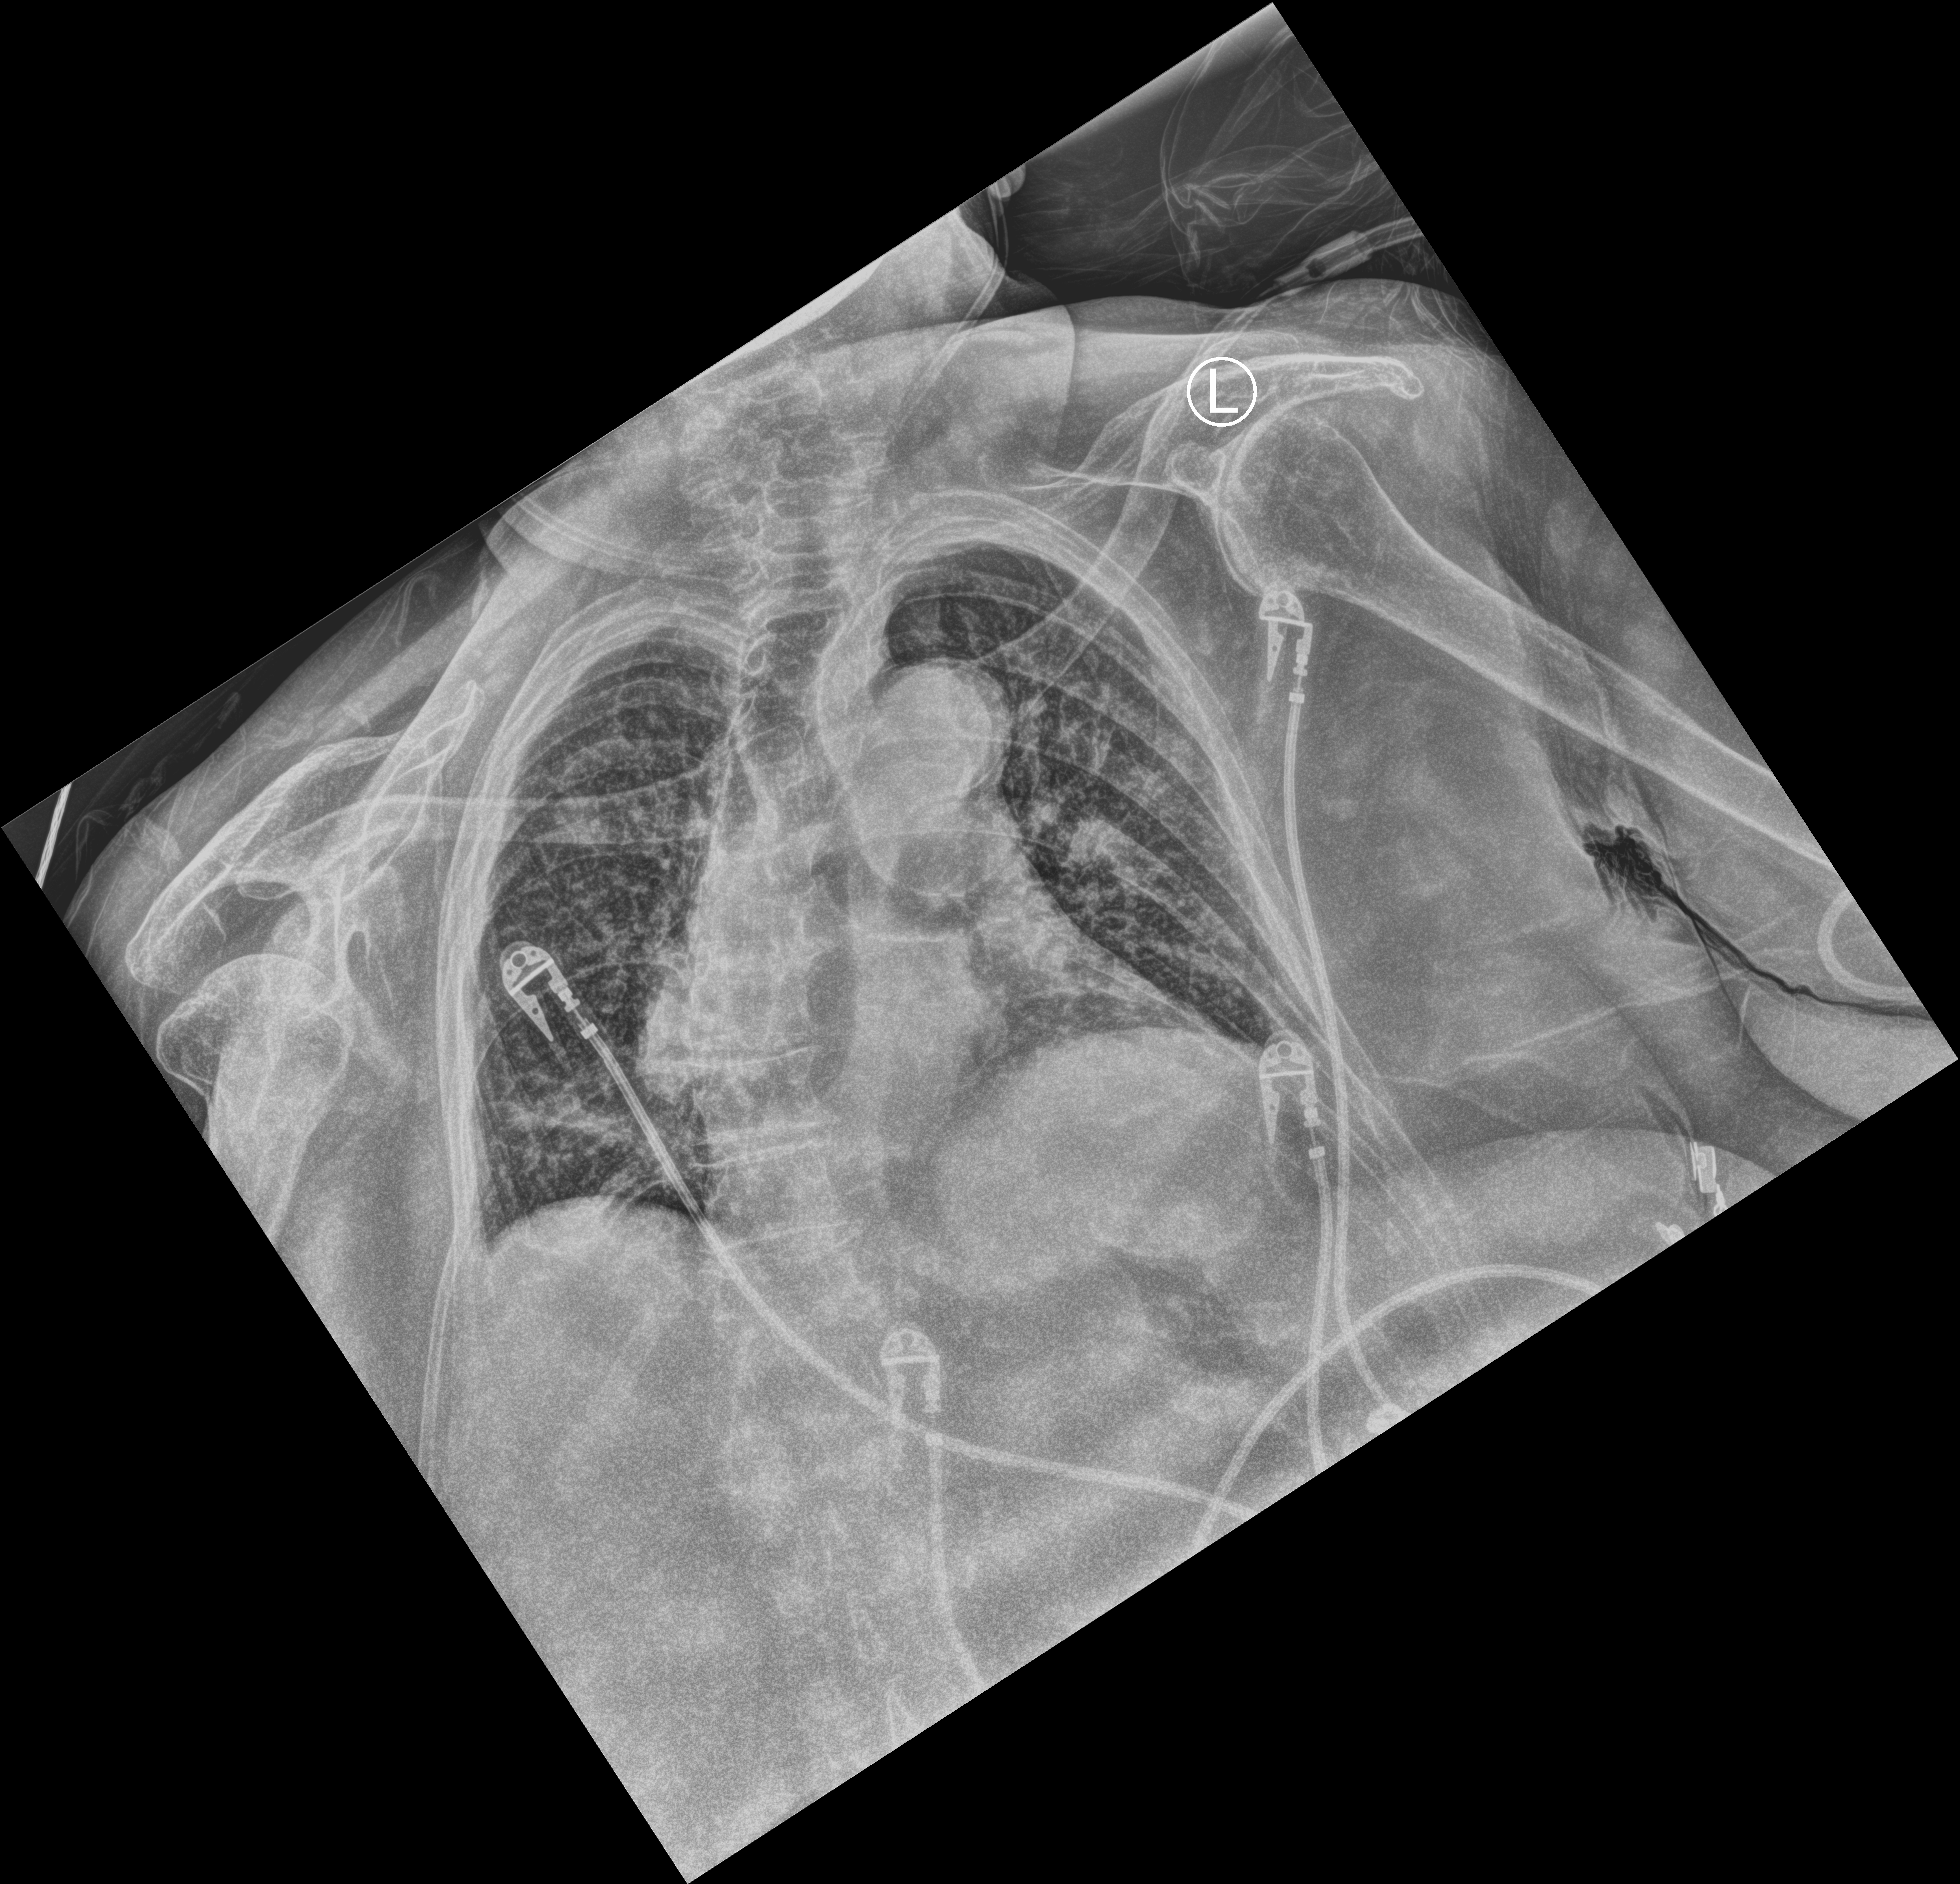
Portable chest radiograph; anteroposterior (AP) projection. Patient hospitalised with COVID-19; female, aged 75–90 years.
Hospital-stay facts (about this admission, not read from this image; timing relative to this image not recorded): length of hospital stay: 12 days; admitted to intensive care during this hospital stay: yes; mechanically ventilated during this hospital stay: no.